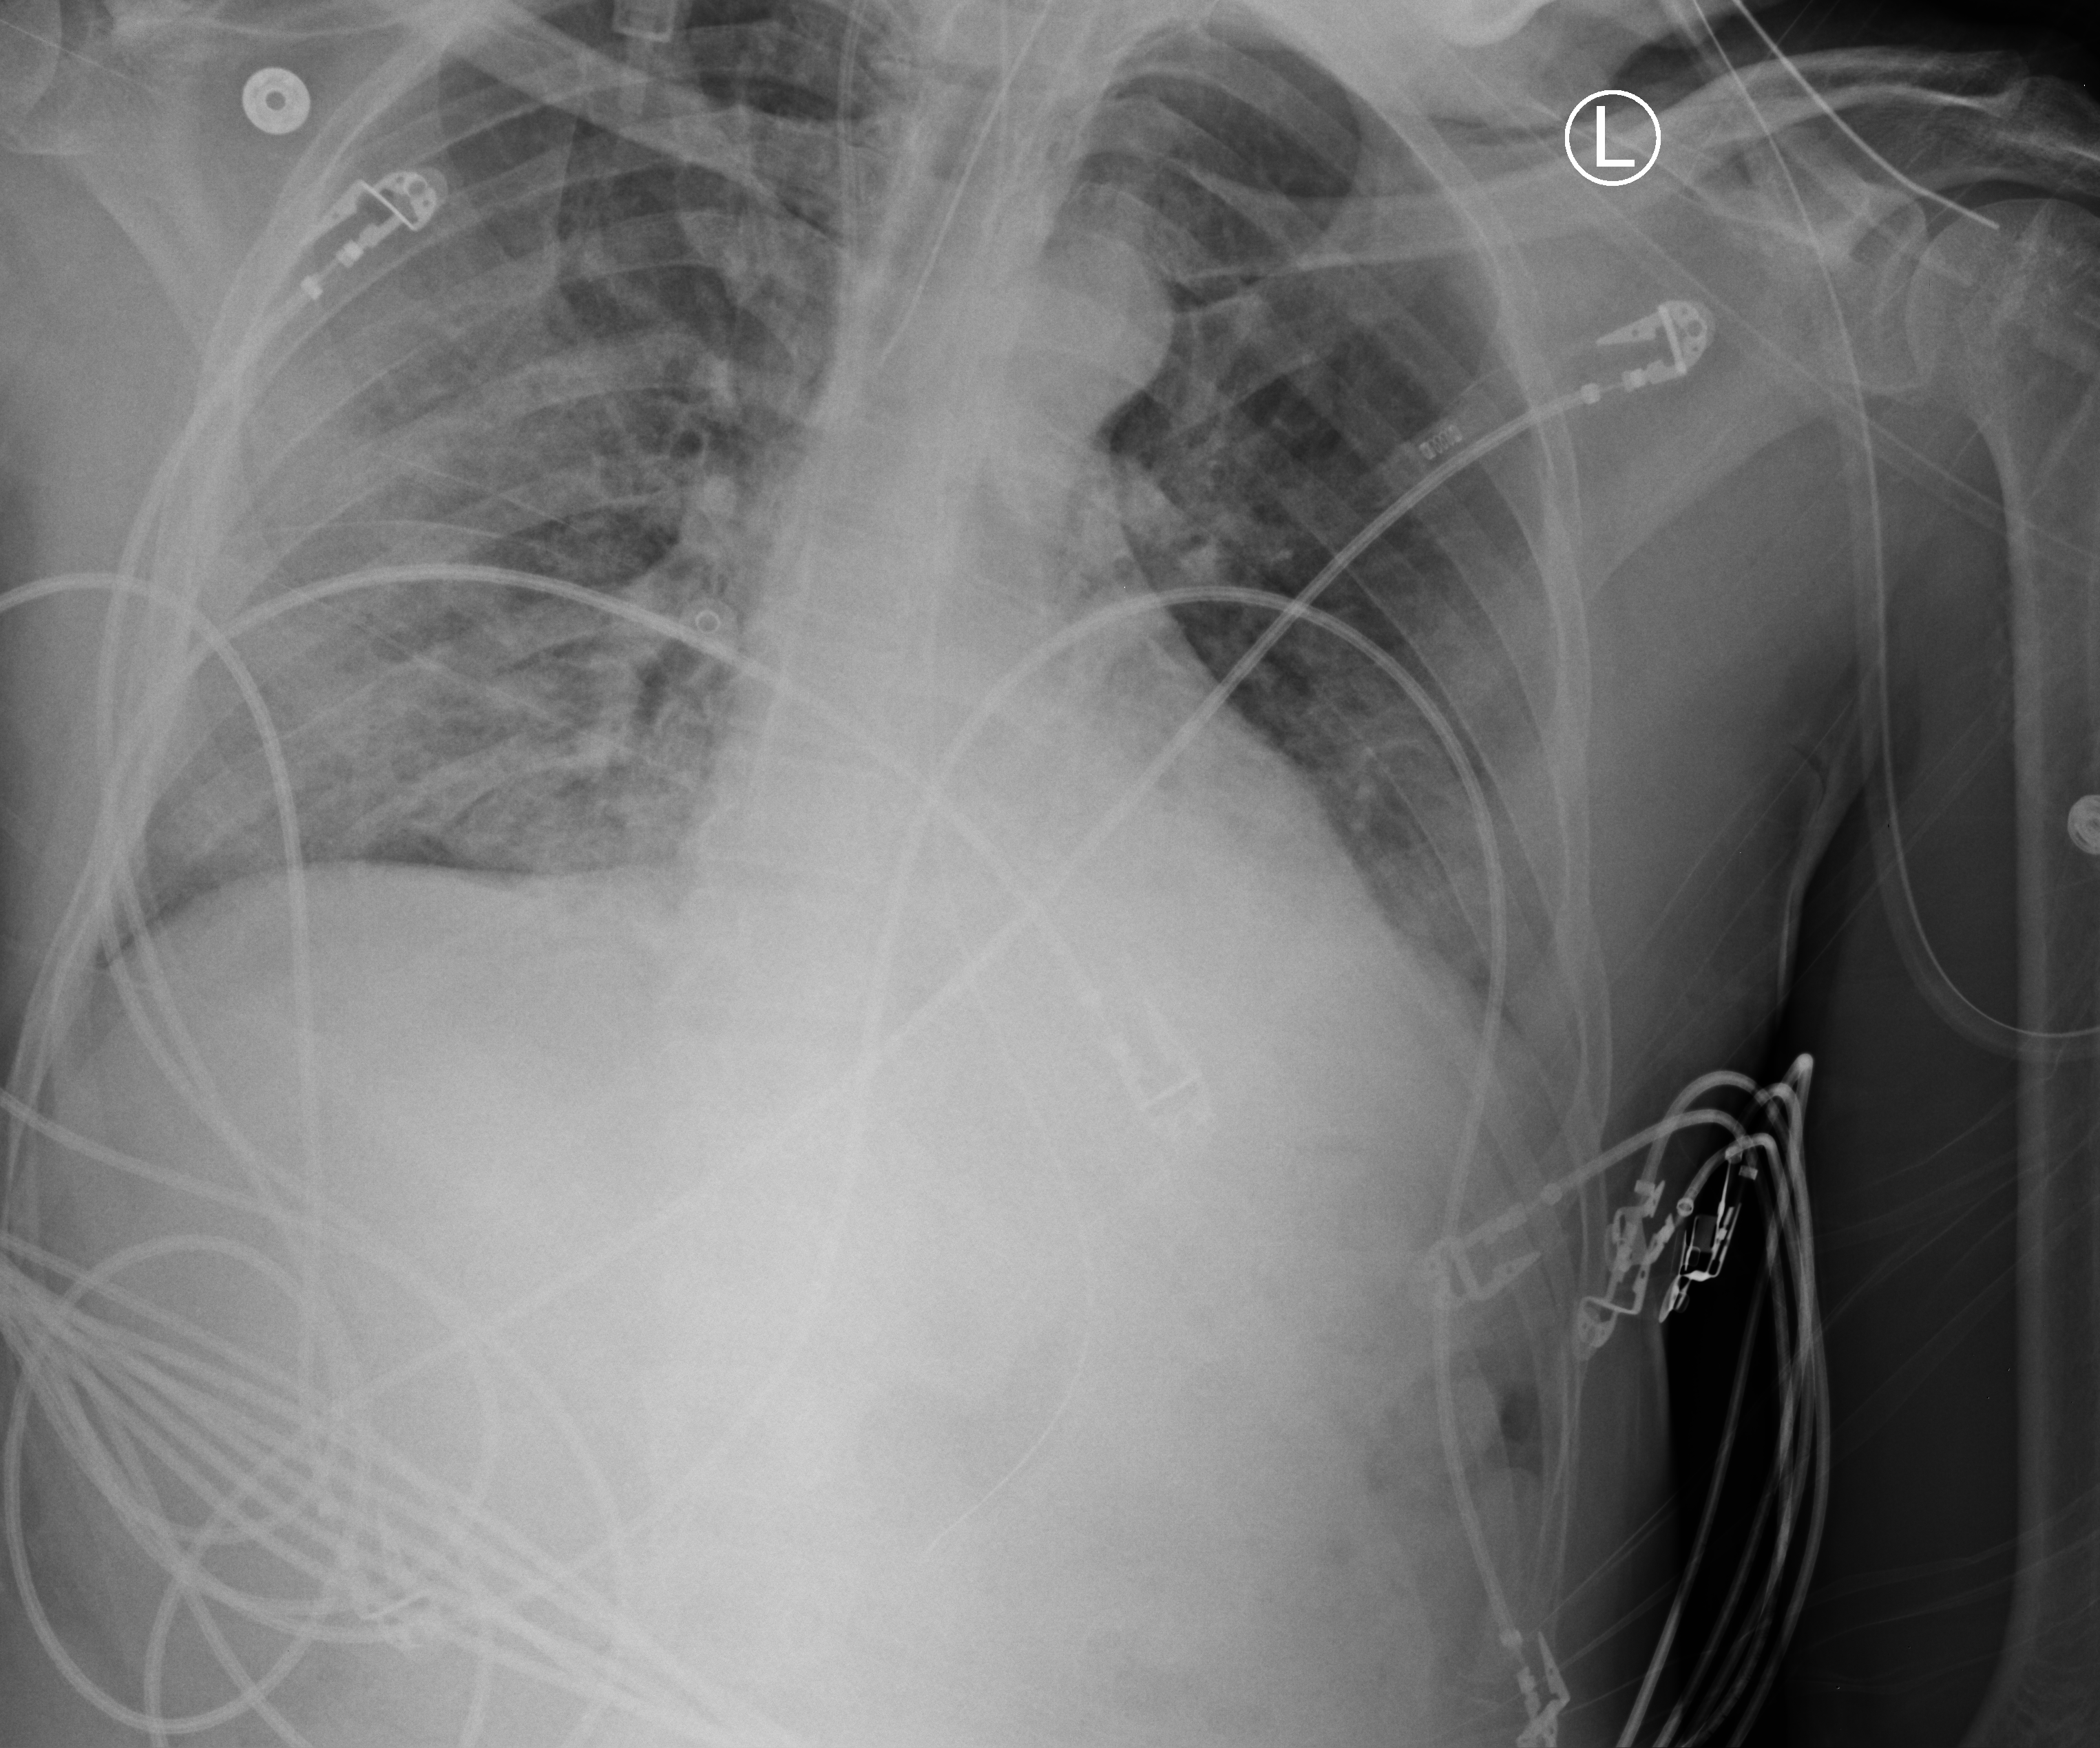
Portable chest radiograph; anteroposterior (AP) projection. Male patient hospitalised with COVID-19, age 18–59 years.
Hospital-stay facts (about this admission, not read from this image; timing relative to this image not recorded): length of hospital stay: 41 days; mechanically ventilated during this hospital stay: yes; admitted to intensive care during this hospital stay: yes.